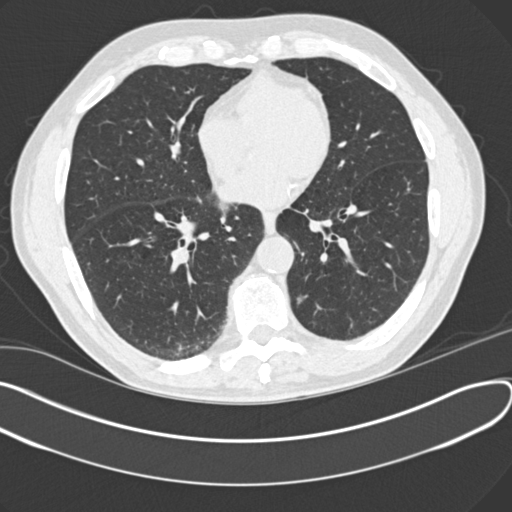
Chest CT (low-dose screening protocol), one axial image. Third annual screen. Lung window (W 1500 / L -600 HU). 2 mm slice thickness. Slice 98 of 166 in the series. 512 × 512 image matrix. Male participant, aged 64 years at enrolment. Former smoker at enrolment.
Expert-annotated lung lesion, bounding box [x1, y1, x2, y2] px = [284, 279, 324, 319]. Reader record for this screening exam (exam-level; its link to the box is not recorded): non-calcified nodule or mass ≥4 mm, left lower lobe, 8 × 7 mm, smooth margins, ground glass attenuation. Lung cancer was diagnosed 39 days after this screen: adenocarcinoma with mixed subtypes, left lower lobe, well differentiated (G1), stage IA (AJCC 6th edition), 7 mm at pathology.